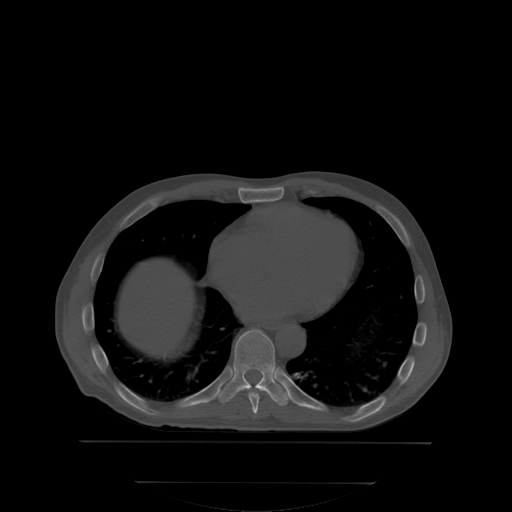
CT including the spine, one axial slice. Position 208 of 350 along the scan axis. Bone window (W 1800 / L 400 HU). 2.5 mm slice thickness. 512 × 512 image matrix, field of view 500 × 500 mm. Male patient, age 58 years. From the clinical record (not read from this slice): primary cancer: prostate; vertebrae with lytic lesions (as recorded): L1.
Annotated regions visible in this slice (semi-automatically segmented with operator editing):
- T8 vertebra: bounding box [x1, y1, x2, y2] px = [248, 391, 259, 414]
- T9 vertebra: [206, 329, 289, 405]